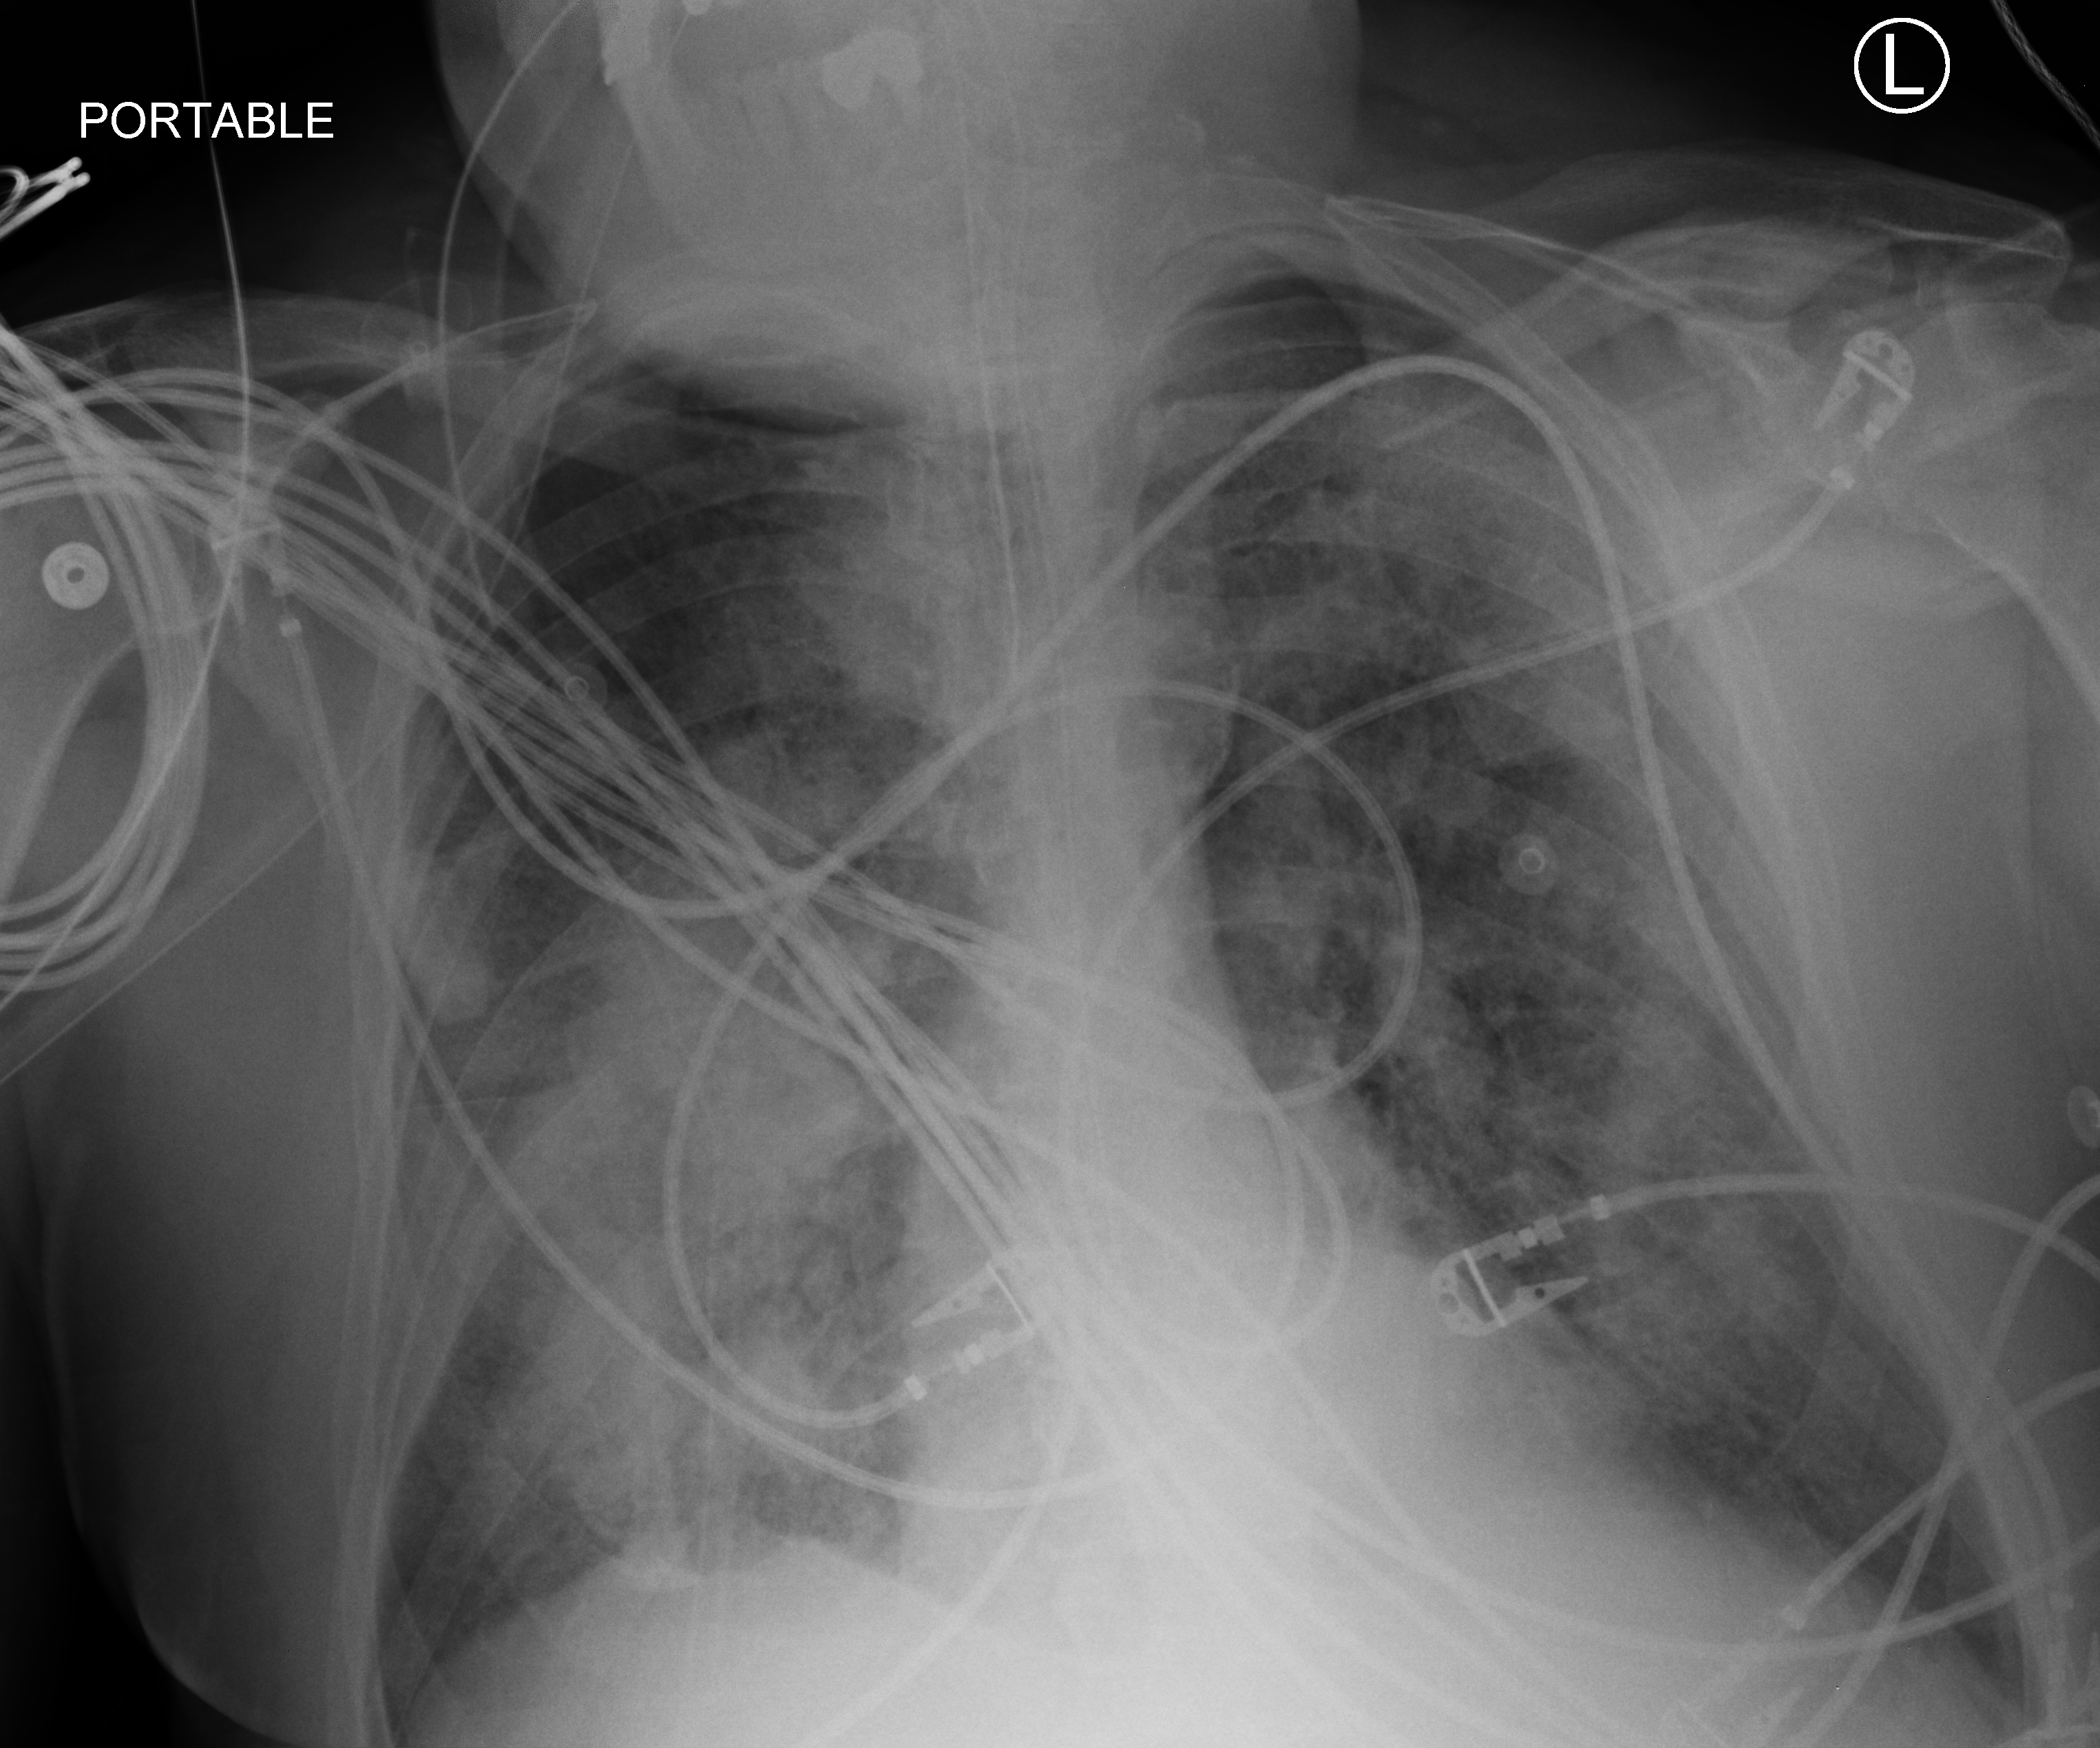
Portable chest radiograph; anteroposterior (AP) projection. Male patient hospitalised with COVID-19, age 60–74 years.
Admission-level facts for this patient (not findings on this image; timing relative to this image not recorded):
- mechanically ventilated during this hospital stay: yes